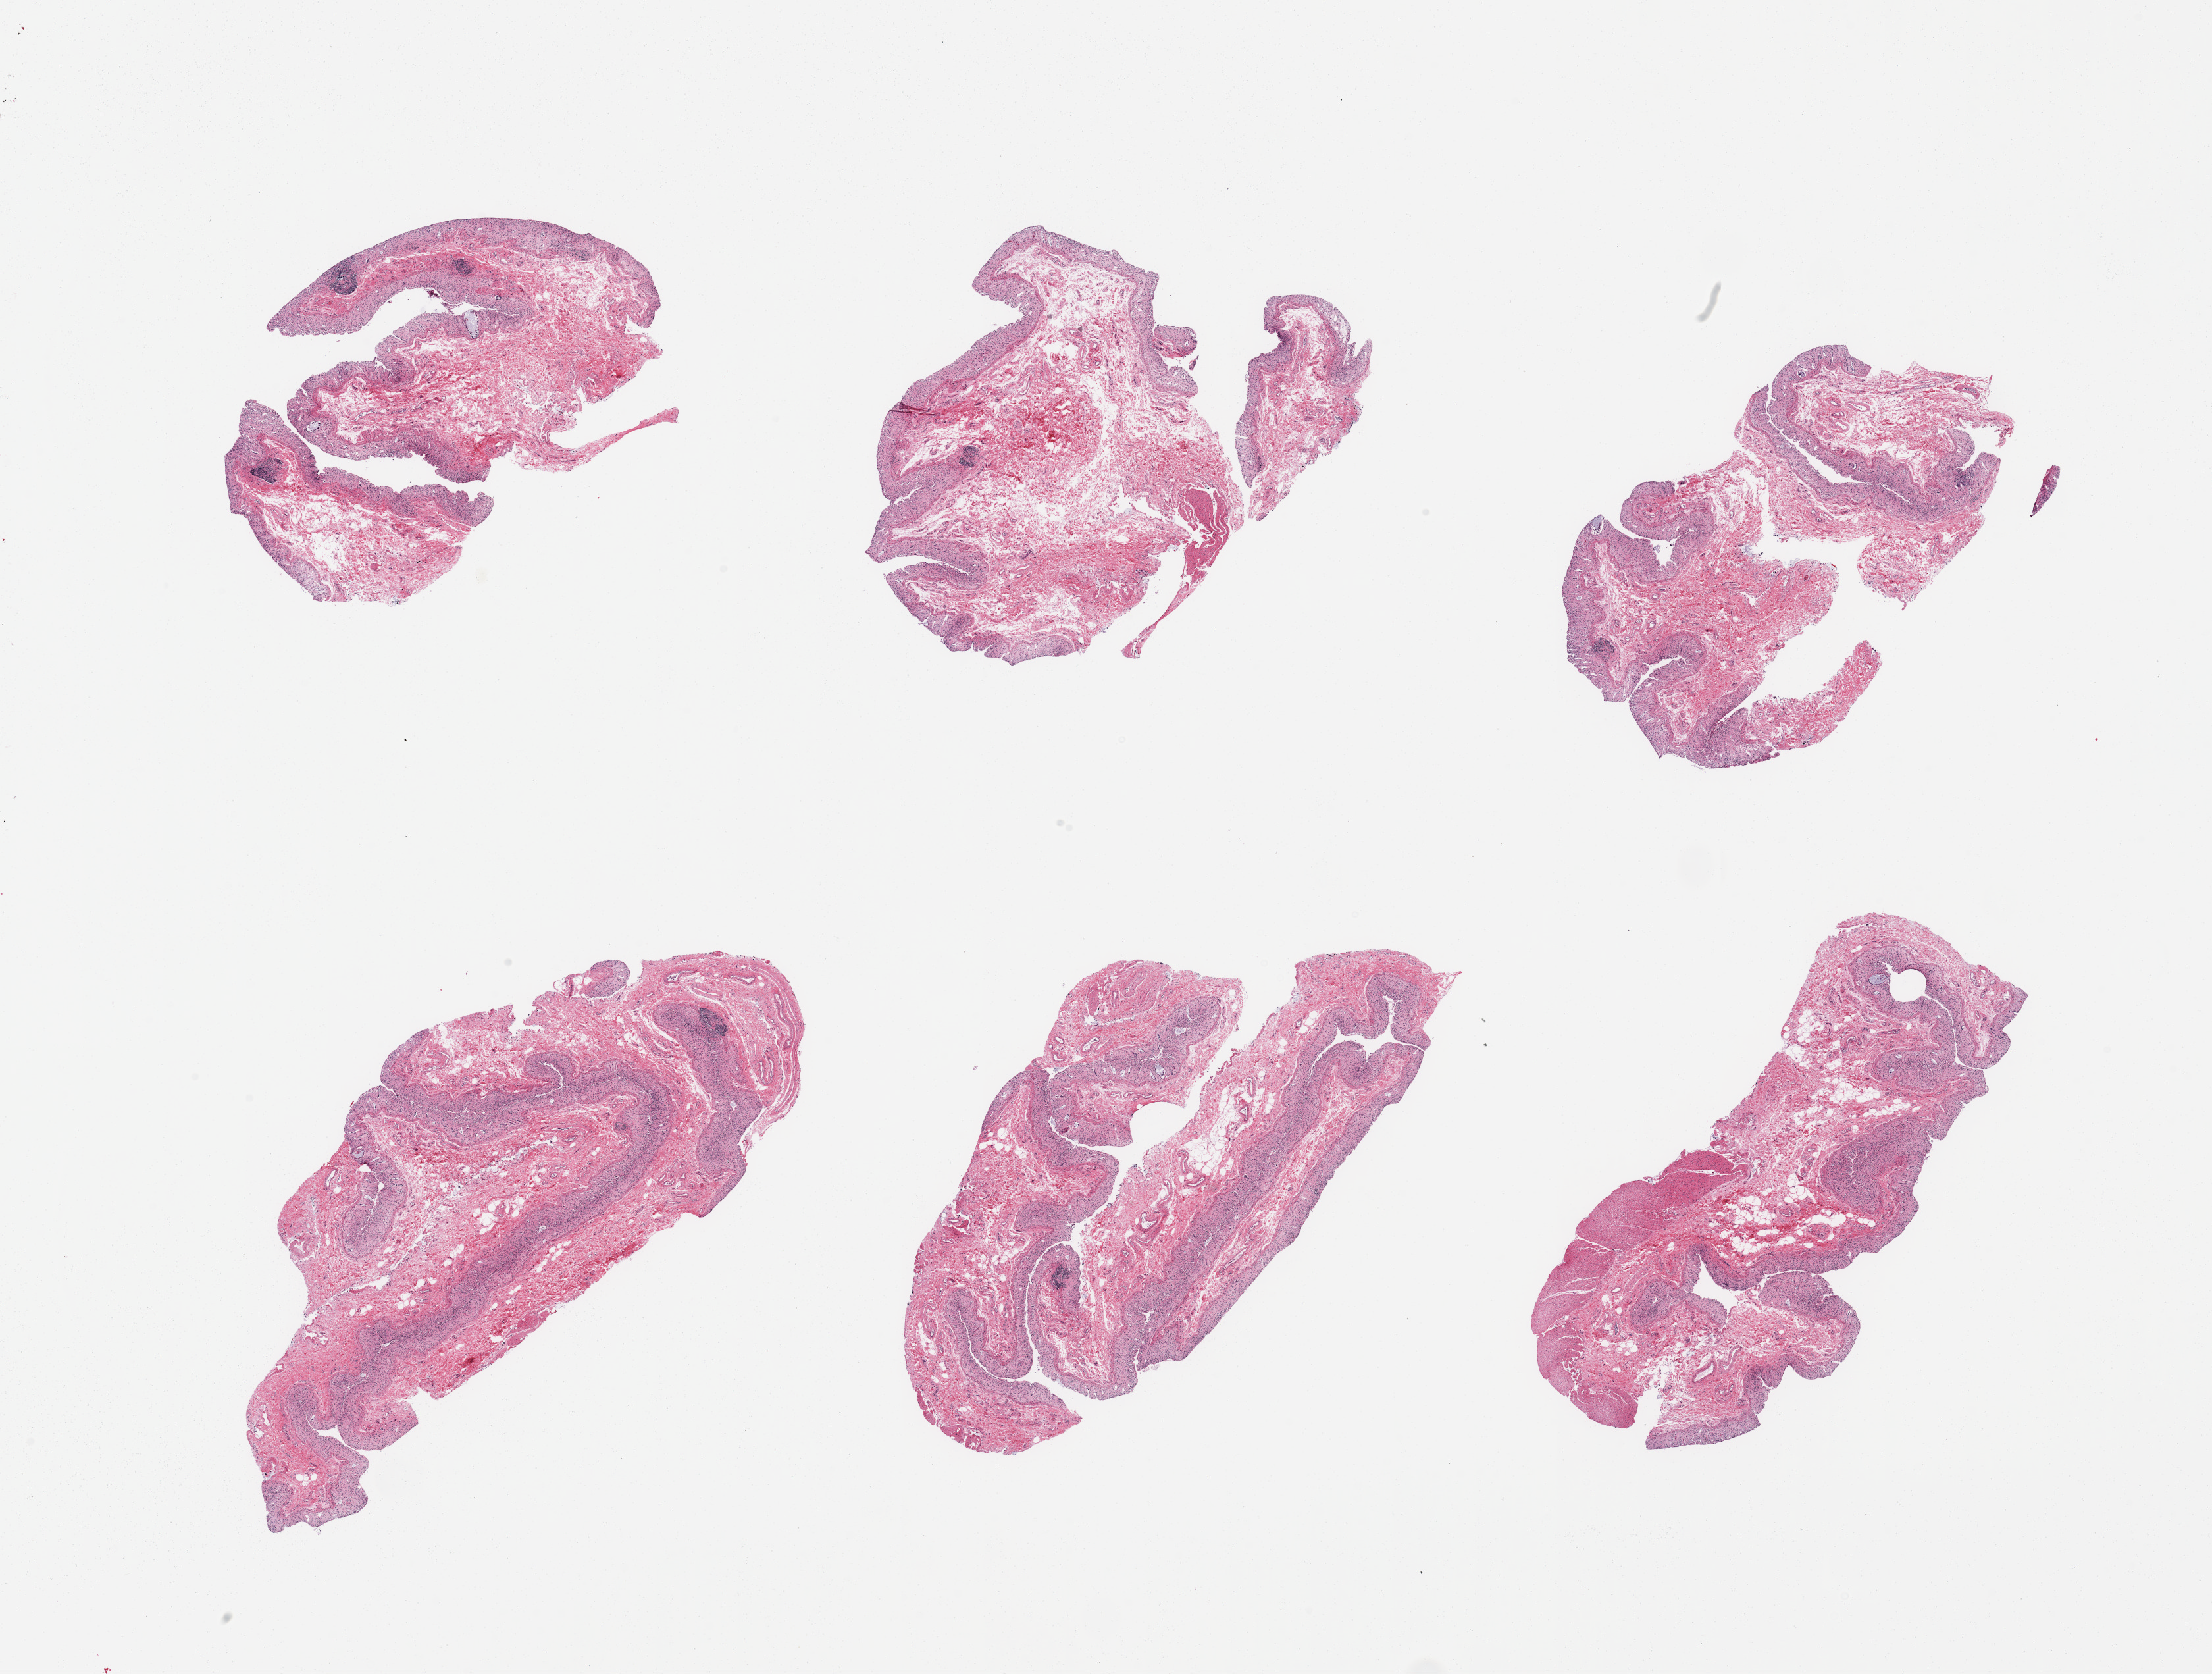
Hematoxylin and eosin (H&E) whole-slide image, a low-resolution overview of the entire scanned area, about 26.6 x 20.1 mm; PAXgene-fixed paraffin-embedded (PFPE) section; target tissue: sigmoid colon; tissue donor sample.
Pathologist's review note for this sample: 6 pieces, advanced autolysis.